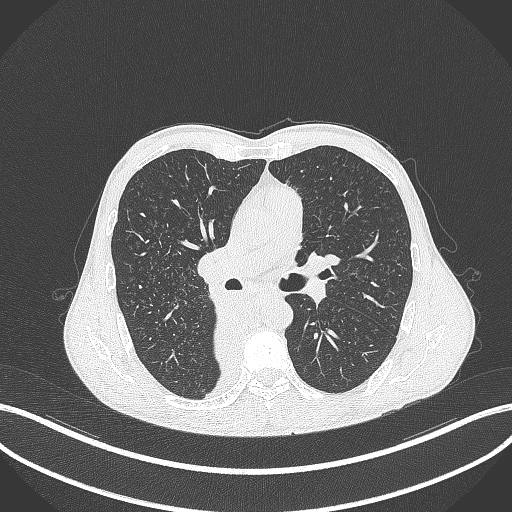
Chest CT, one axial slice; position 221 of 371 along the scan axis; reconstruction kernel B70f; lung window (W 1500 / L -600 HU); 512 × 512 image matrix. Male patient, age 58 years. Case-level facts recorded for this patient, not image findings: clinical TNM (as recorded): T3 N1 M1.
Outlined on this slice (bounding box drawn by a radiologist):
- lung tumour (recorded histology: squamous cell carcinoma): box from (x=198, y=291) to (x=269, y=388) px